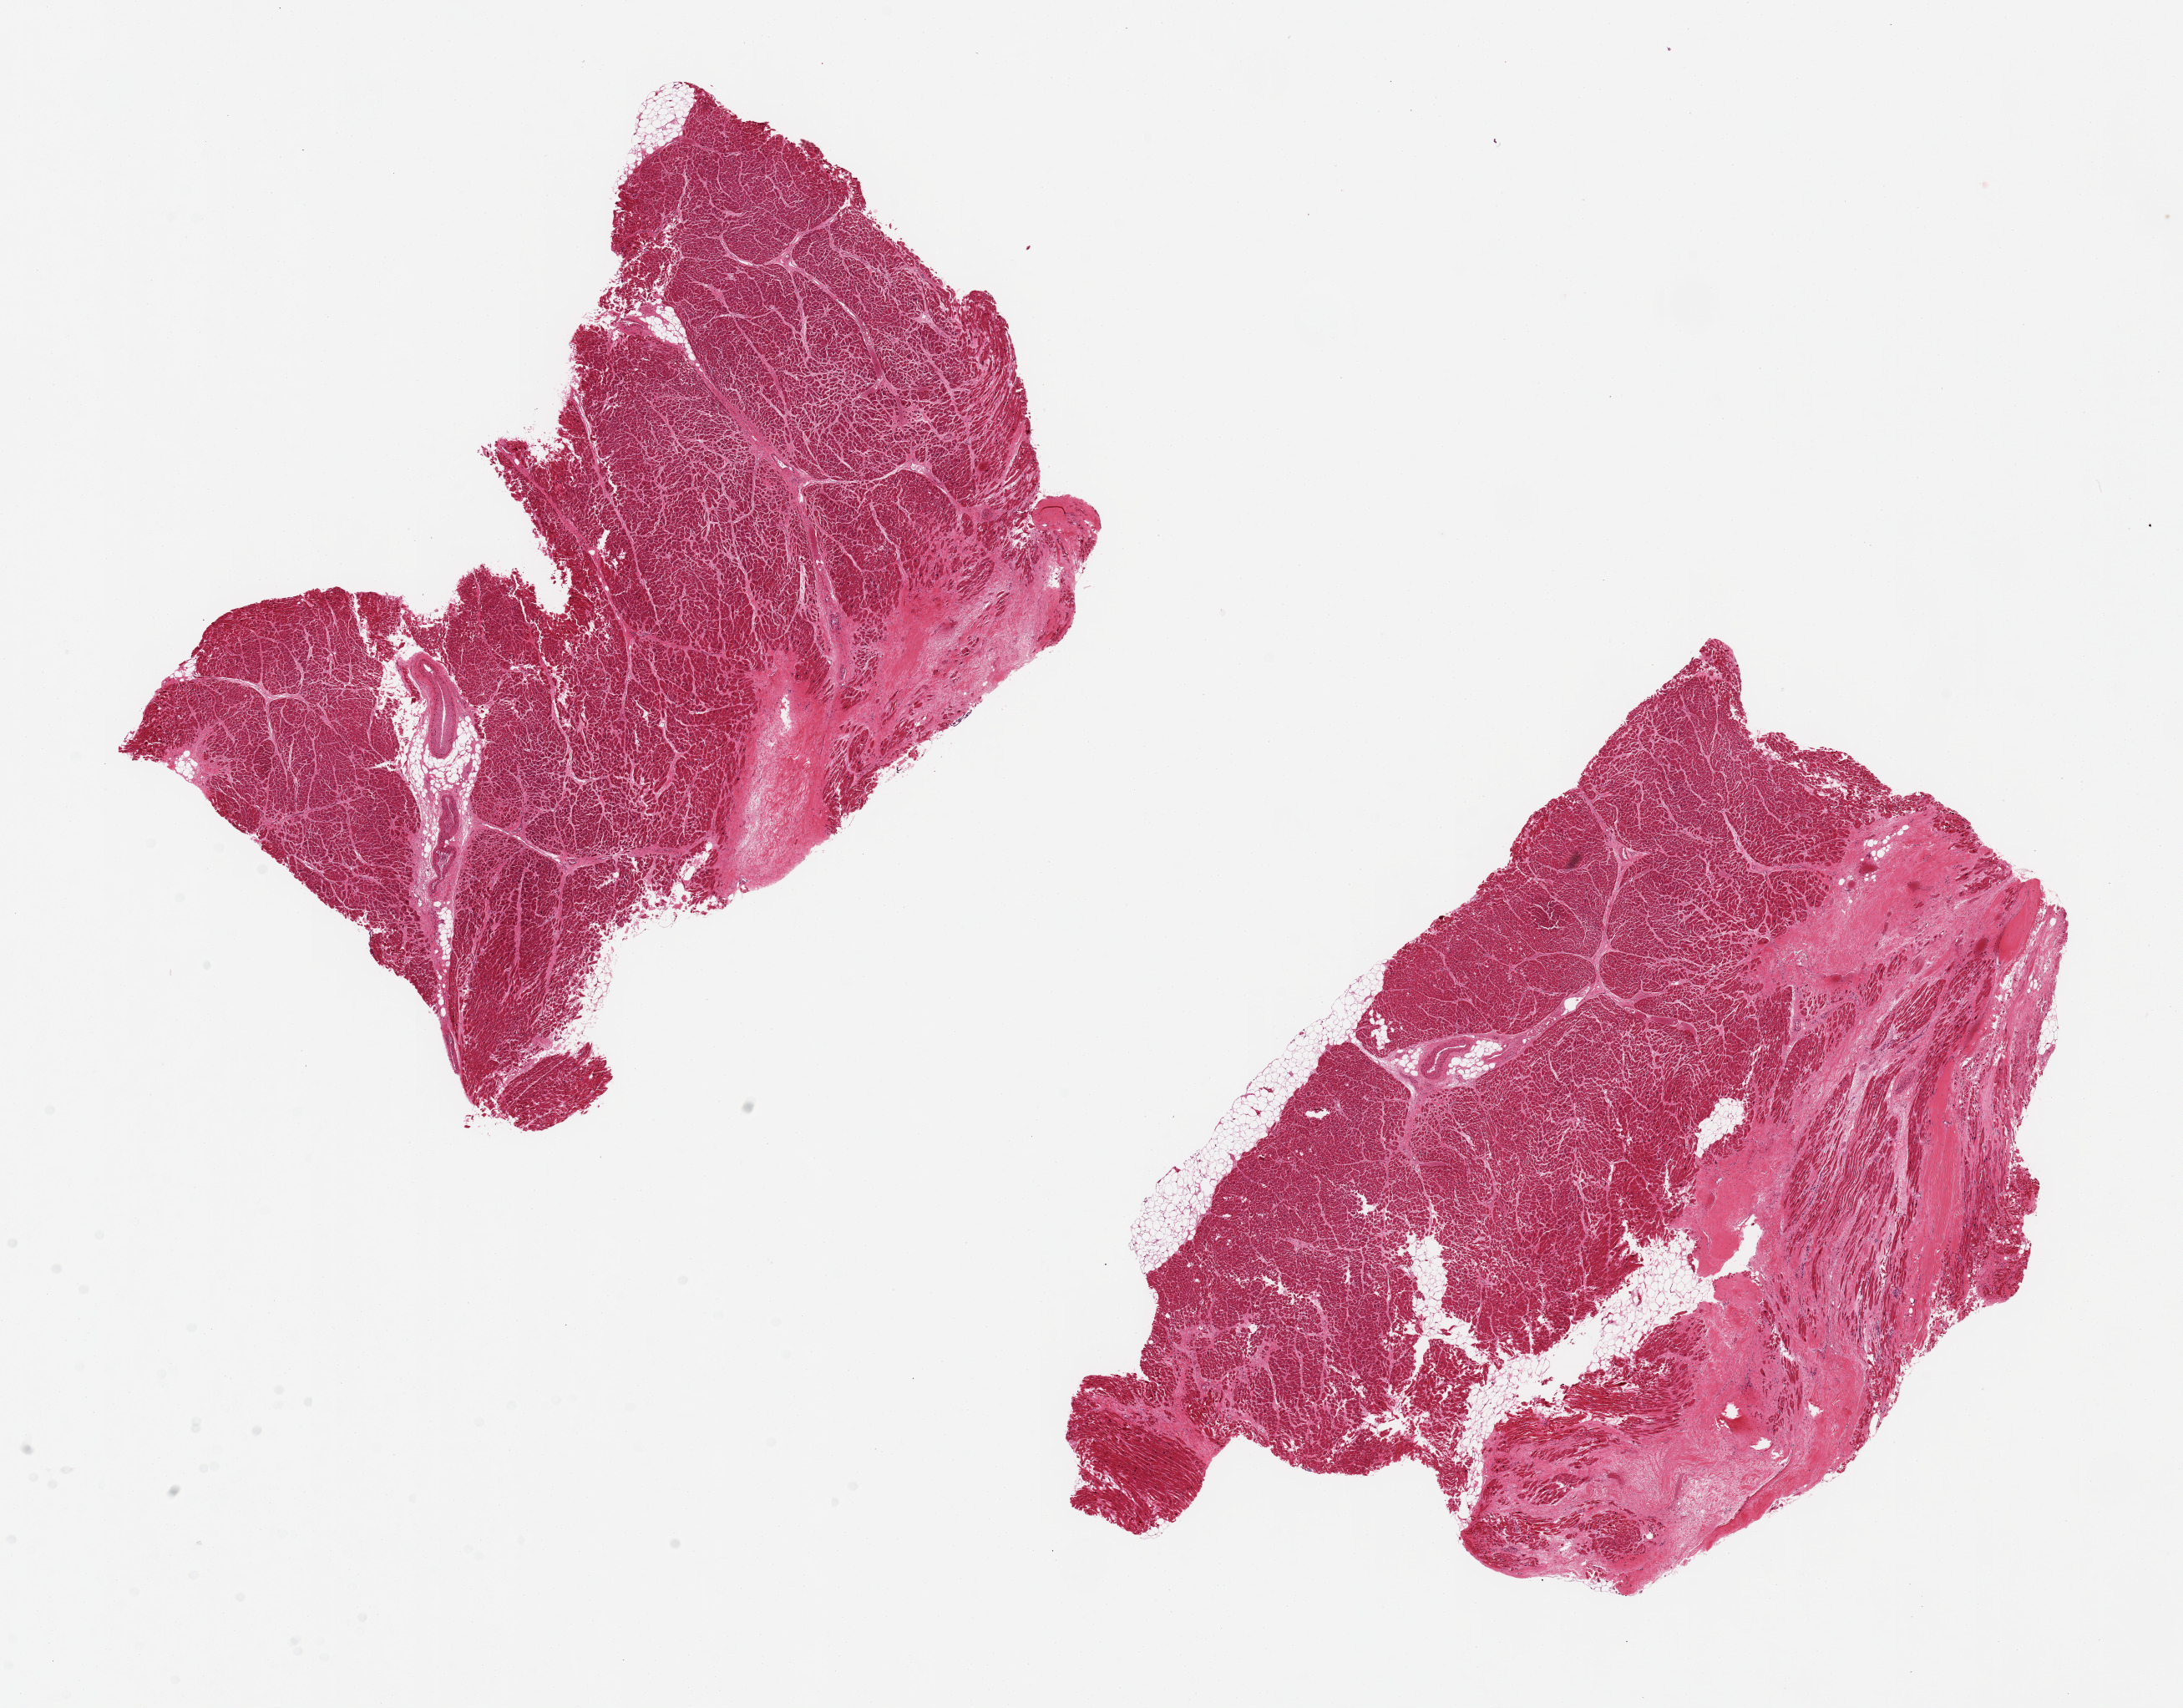
Whole-slide image, hematoxylin and eosin (H&E) stain, whole scanned area (about 20.7 x 16.2 mm) shown as a low-resolution overview, PAXgene-fixed, paraffin-embedded tissue, sampled site (target tissue): heart, donor tissue sample.
Pathologist's review note for this sample: 2 aliquots, ~9x5mm; Confluent foci of remote fibrotic infarcts up to 7x3mm in dimensions.